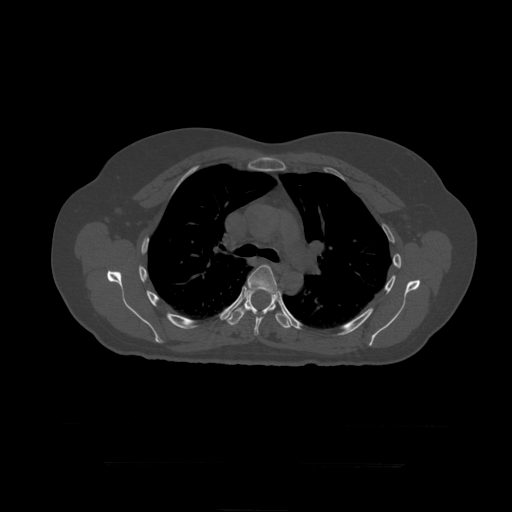
CT including the spine, one axial slice. Position 311 of 399 along the scan axis. Reconstruction kernel STANDARD. 120 kVp. Bone window (W 1800 / L 400 HU). 1.25 mm slice thickness. 512 × 512 image matrix. Patient age 41 years. From the clinical record (not read from this slice): primary cancer: breast.
Outlined on this slice (semi-automatically segmented with operator editing):
- T6 vertebra: bounding box <246,265,278,336> (left, top, right, bottom; pixels)
- T7 vertebra: <226,289,292,329>